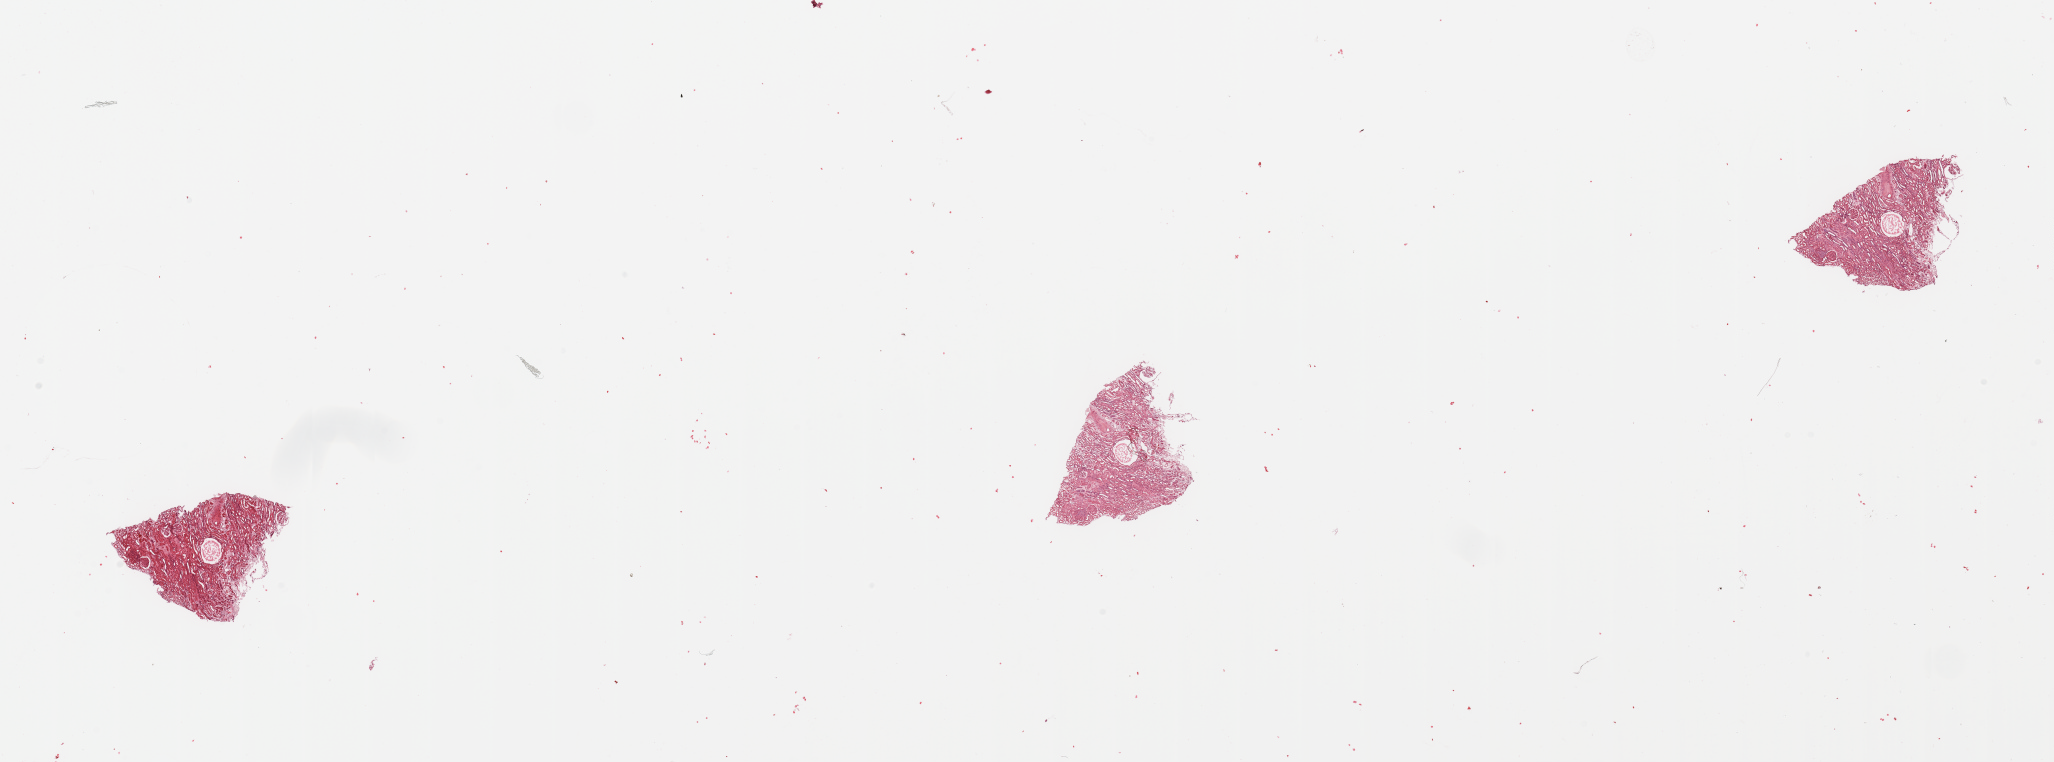
Digitized H&E tissue section (whole slide), low-resolution overview of the scanned area, about 32.5 x 12.1 mm (acquisition: 20x scan). Normal (non-tumour) tissue sample, sampled site: kidney. 63-year-old male patient.
This section: normal (non-tumour) tissue from the same patient. Patient diagnosis: Renal cell carcinoma, NOS.